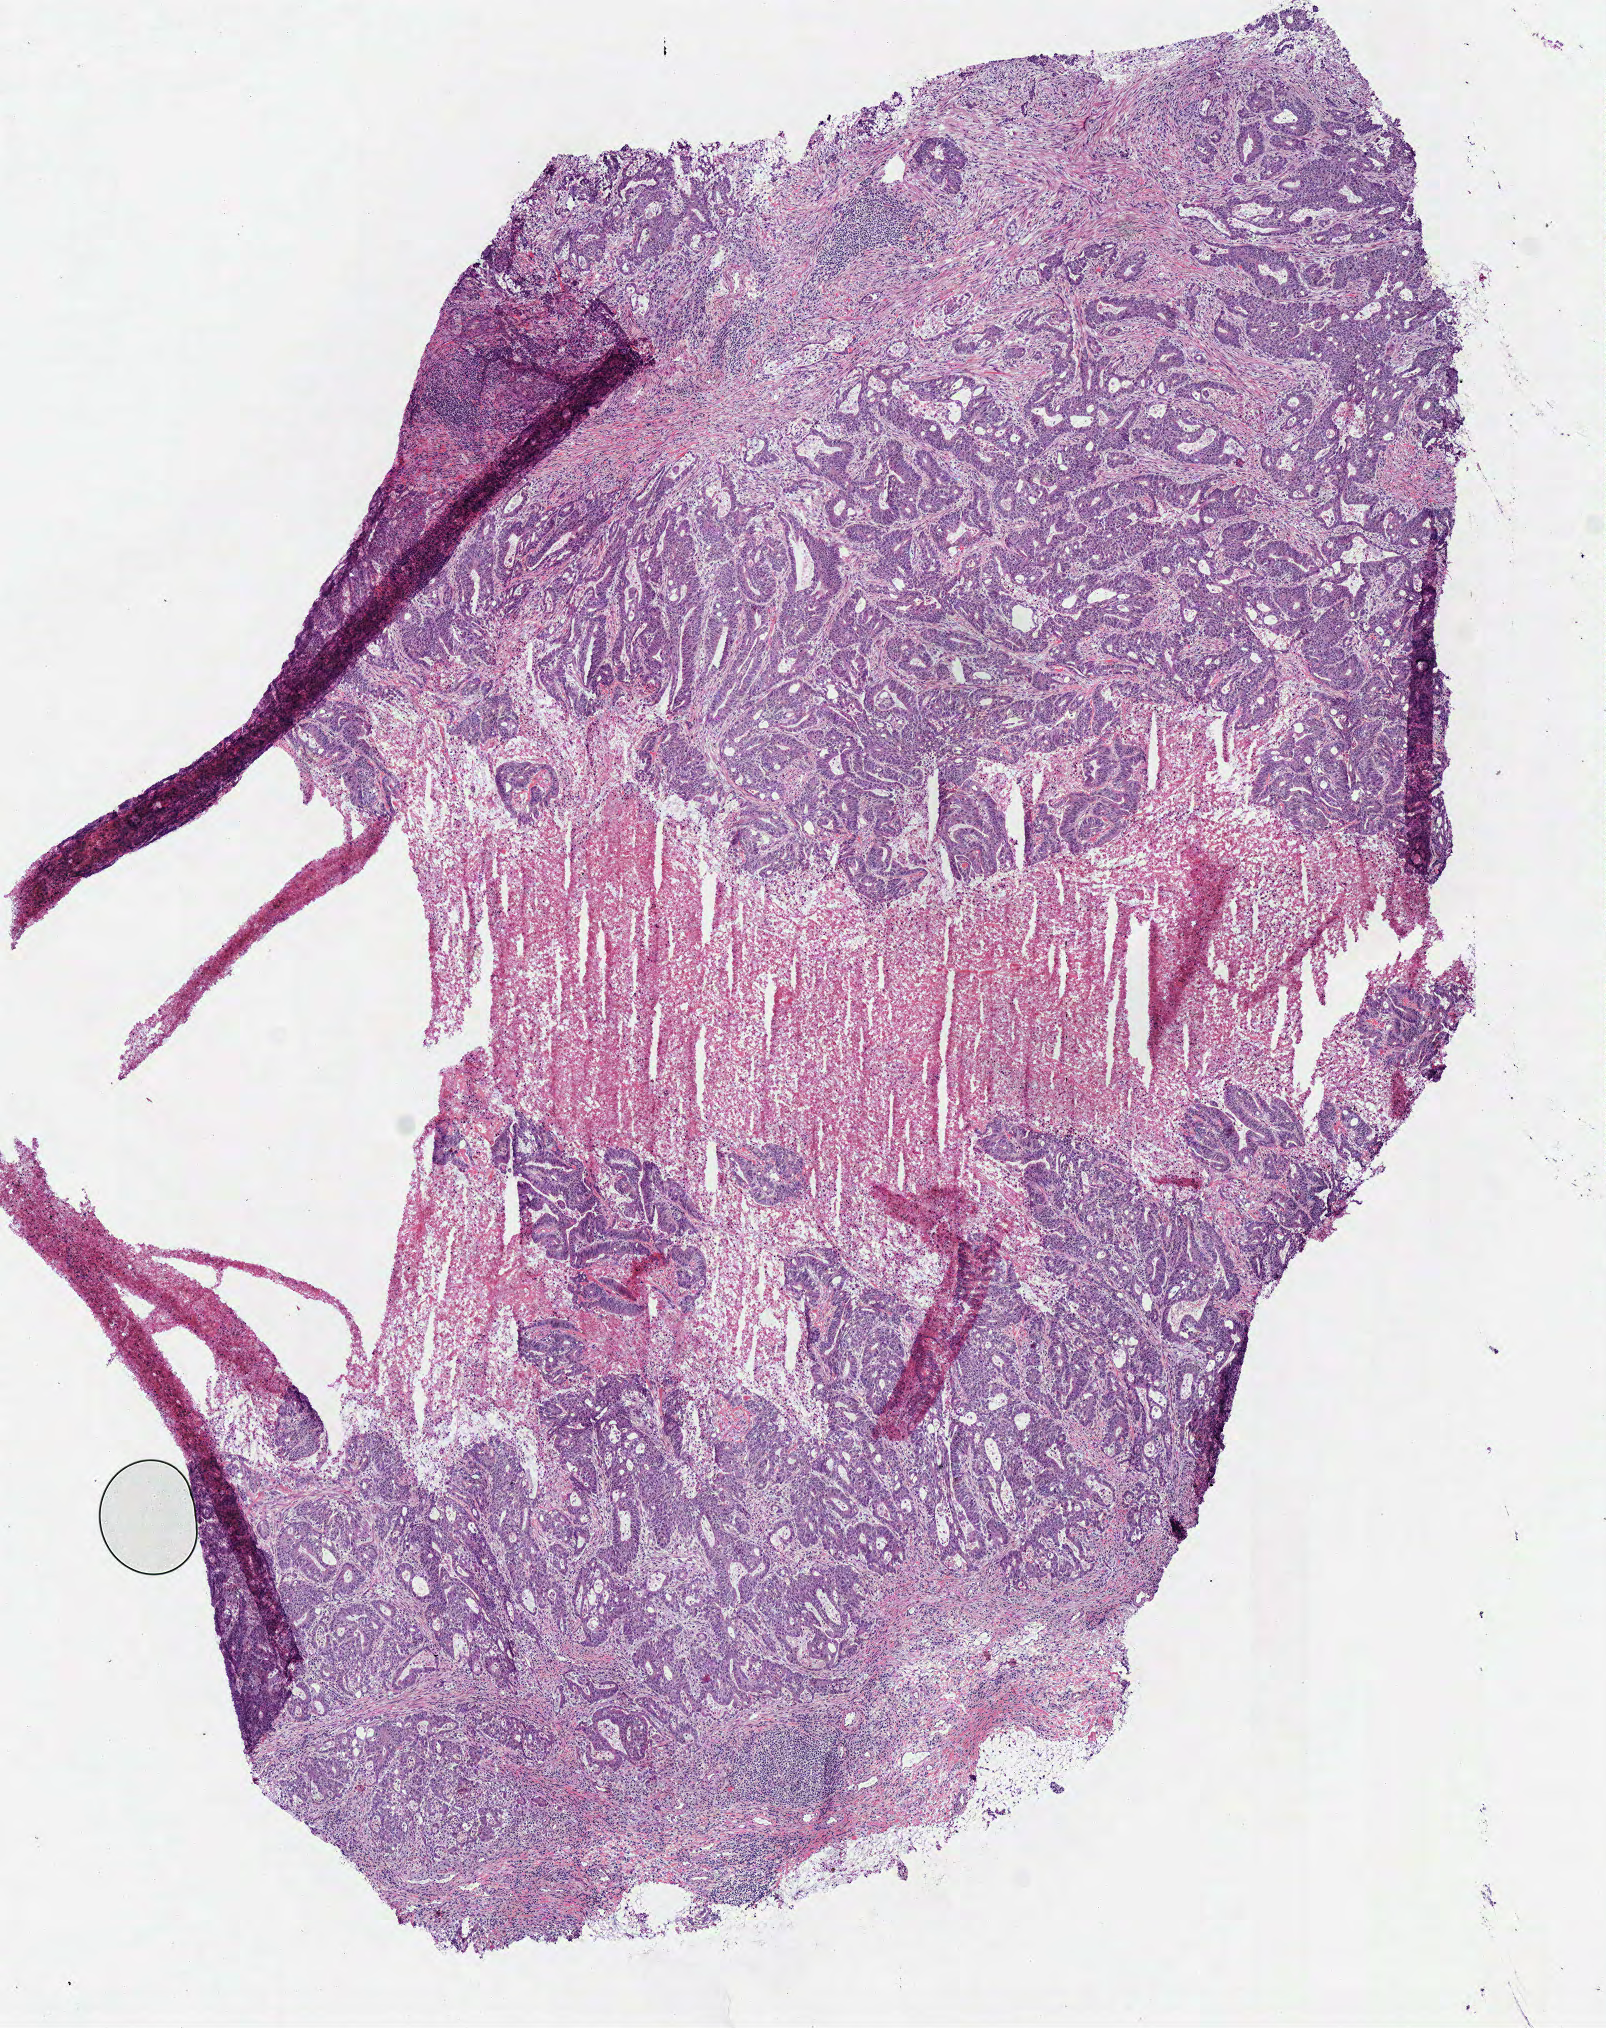
Whole-slide histology image, H&E, low-resolution overview of the scanned area, about 6.3 x 8.0 mm, frozen section from the bottom of the tissue portion, sample: primary tumour, colon. Patient: male, age at initial diagnosis 77 years. Slide review estimates, as recorded: tumour cells 48%, tumour nuclei 65%, normal cells 0%, stromal cells 37%, necrosis 15%. Infiltration values recorded for this section: lymphocyte infiltration 12%, monocyte infiltration 0%, neutrophil infiltration 2%.
TNM: T4b N2 M0. AJCC pathologic stage: IIIC. Histologic diagnosis: Adenocarcinoma, NOS.